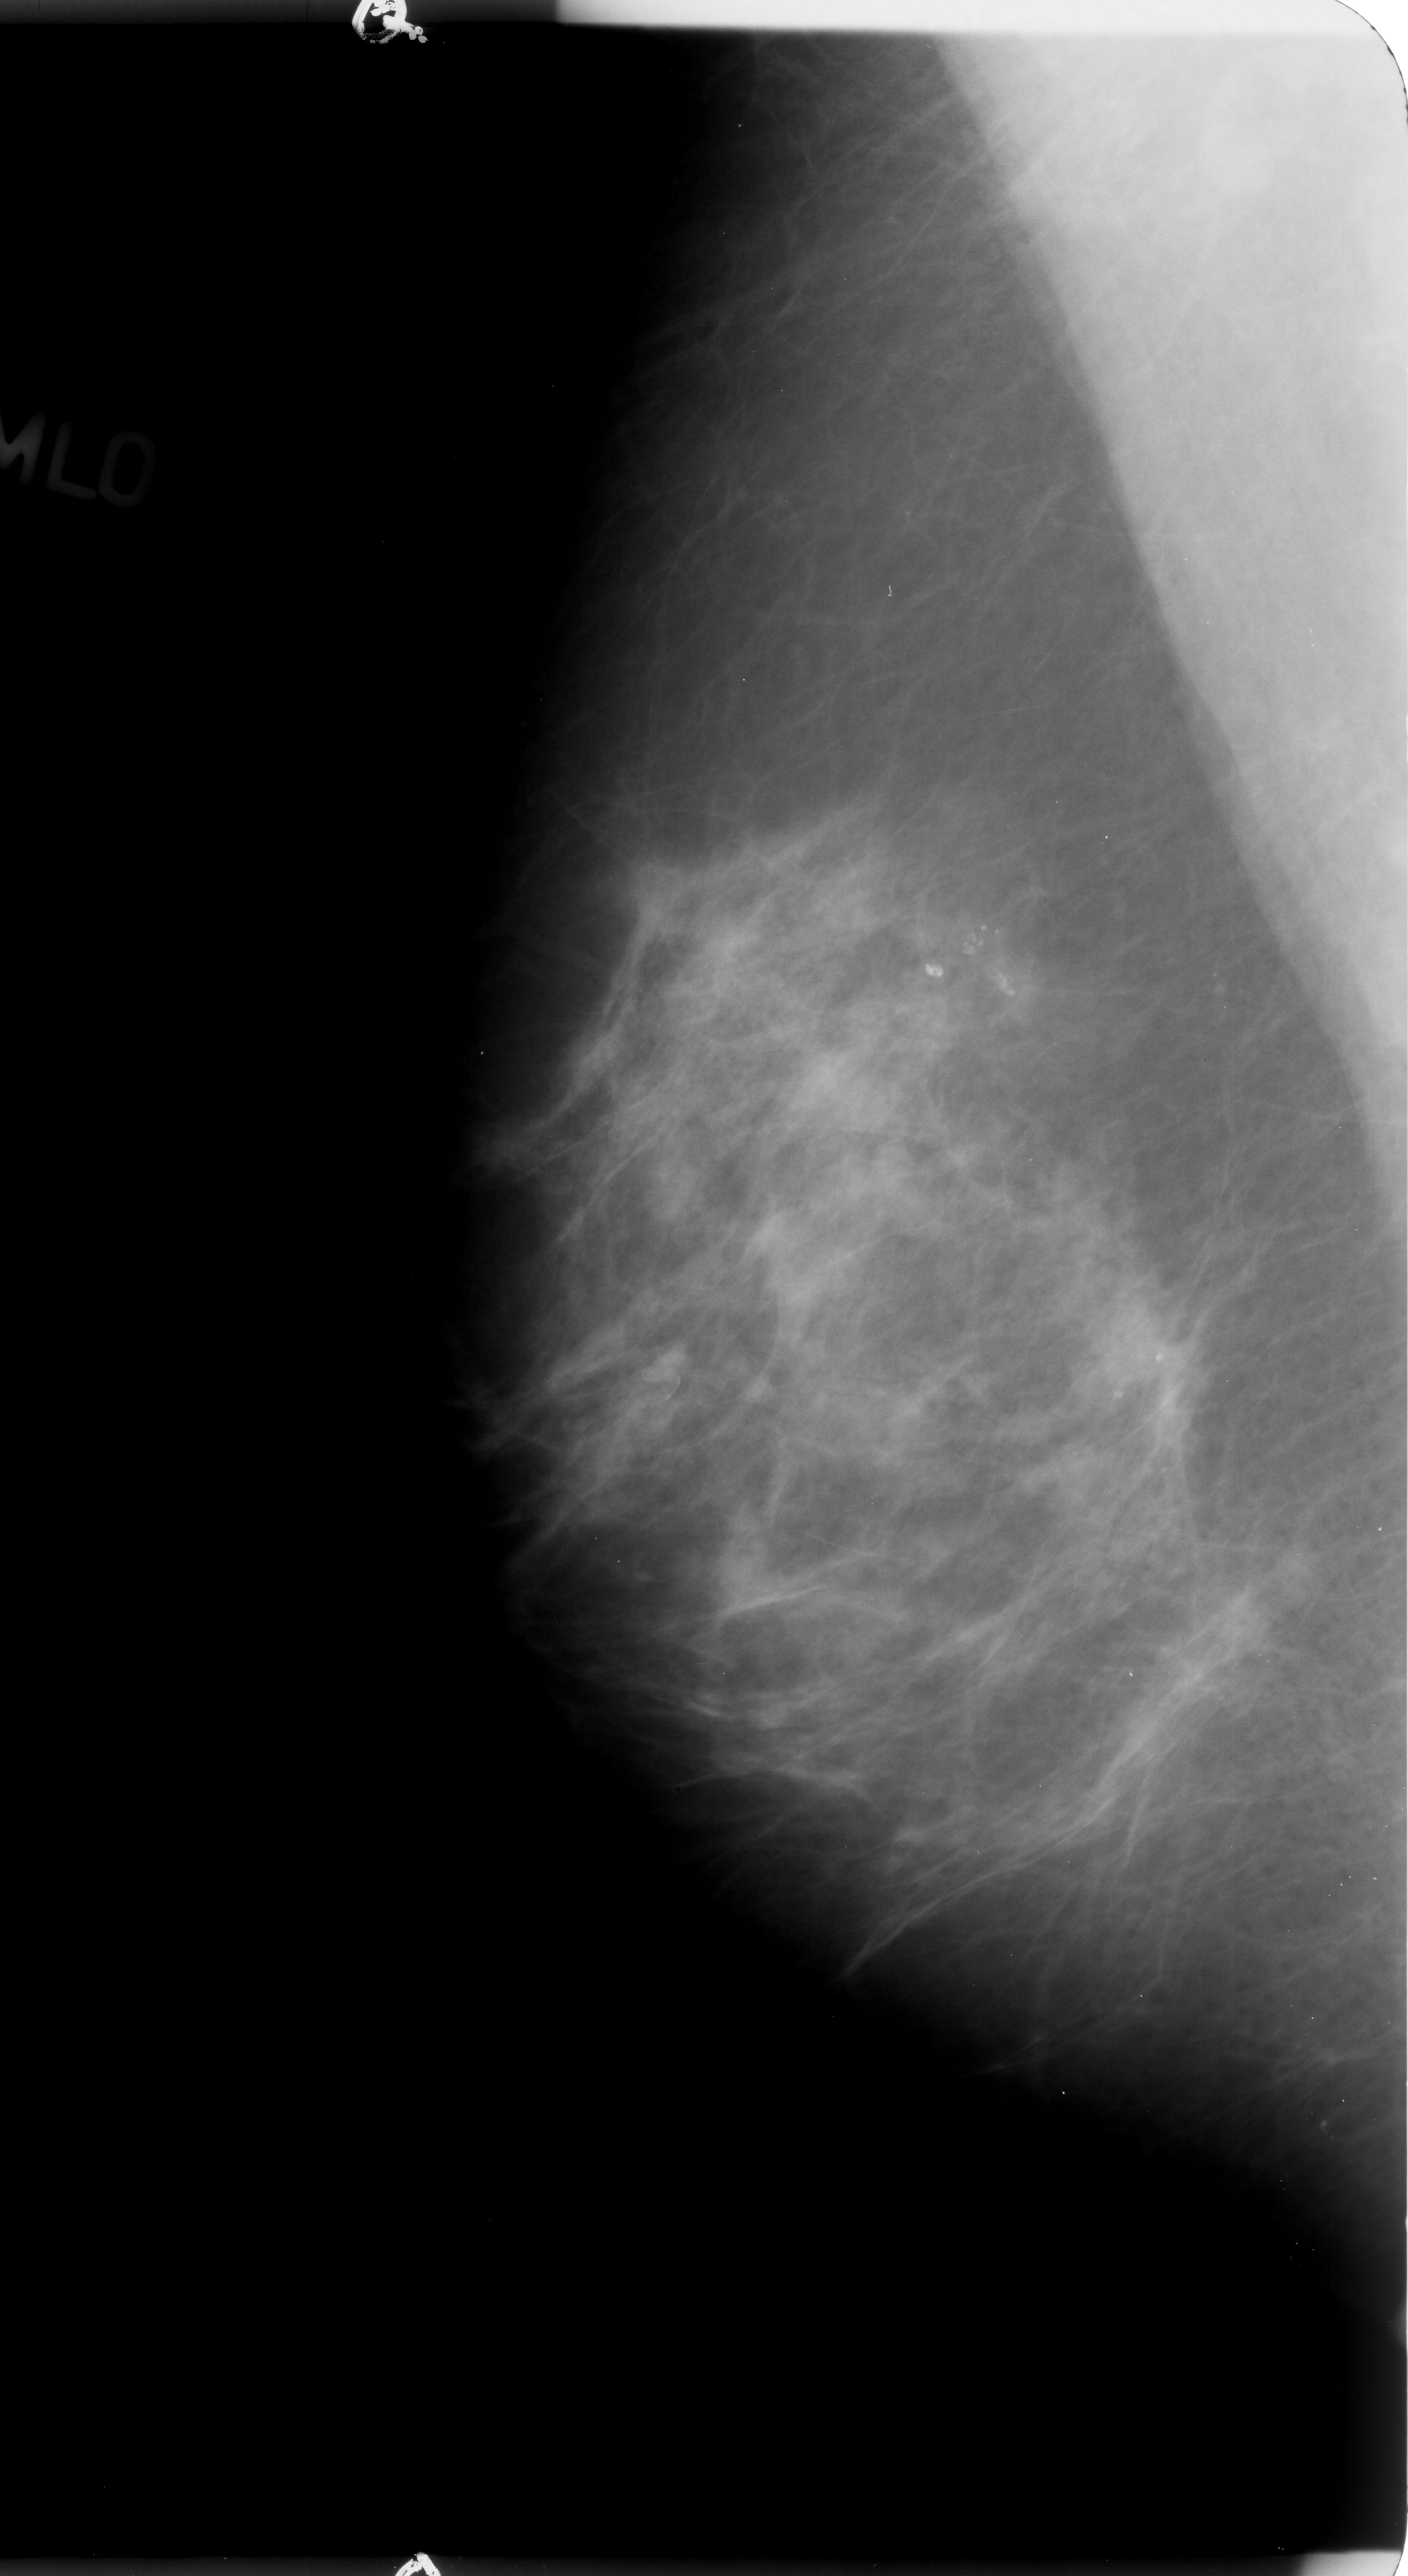
Mammogram (digitized film); right breast; mediolateral oblique (MLO) view; BI-RADS breast density category 2 (scale 1–4); 1408 × 2576 image matrix.
Expert-marked regions of interest on this film, with their recorded descriptors:
- calcifications, morphology pleomorphic, distribution clustered; BI-RADS assessment category 4; subtlety rating 4 on a 1 (subtle) to 5 (obvious) scale; pathology result (as recorded, not read from the image): benign: bounding box [x1, y1, x2, y2] px = [850, 854, 1090, 1081]